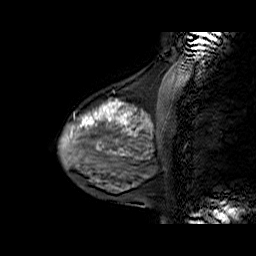
Breast MRI (dynamic contrast-enhanced), one sagittal slice; position 21 of 60 along the scan axis; dynamic contrast-enhanced series, time point 2 of 6 at this slice position (early post-contrast); 1.5 T; TE 6.3 ms, TR 32.9 ms; 256 × 256 image matrix. Female patient. From the clinical record (not read from this slice): setting: breast cancer imaged before/during neoadjuvant chemotherapy; receptor status: HR-positive, HER2-negative.
Structures marked on this image (semi-automatically segmented with operator editing):
- analysis volume of interest (the breast-tissue region the enhancement analysis was run in; not a lesion): bounding box [x1, y1, x2, y2] px = [60, 86, 169, 170]
- tumour enhancement mask (voxels above the 100 % enhancement threshold inside the analysis volume of interest): [71, 100, 150, 136]